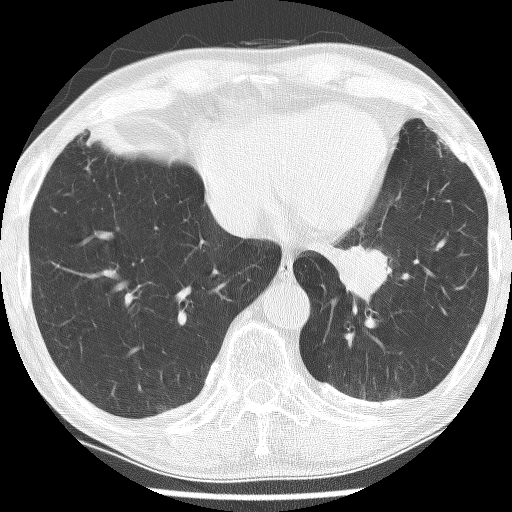
Low-dose screening chest CT, one axial slice; position 49 of 226 along the scan axis; reconstruction kernel BONE; 120 kVp; lung window (W 1500 / L -600 HU); 2.5 mm slice thickness; 512 × 512 image matrix, field of view 320 × 320 mm.
Structures marked on this image (manually delineated by an expert):
- lesion 1 (tumor, lower lobe of left lung): bounding box <339,244,392,303> (left, top, right, bottom; pixels)